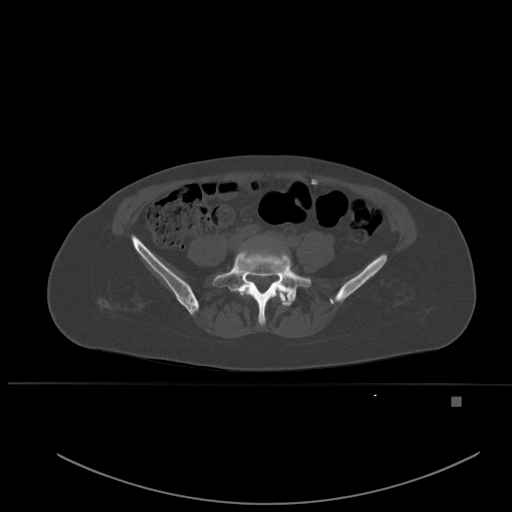
CT including the spine, one axial slice. Slice 158 of 651 in the series (ordered by position). Bone window (W 1800 / L 400 HU). 1.5 mm slice thickness. 512 × 512 image matrix, field of view 443 × 443 mm. Patient: female, 49 years. From the clinical record (not read from this slice): primary cancer: breast.
Annotated regions visible in this slice (semi-automatic segmentation, software-assisted and operator-edited):
- L4 vertebra: bounding box [x1, y1, x2, y2] px = [240, 287, 287, 302]
- L5 vertebra: [212, 250, 311, 325]